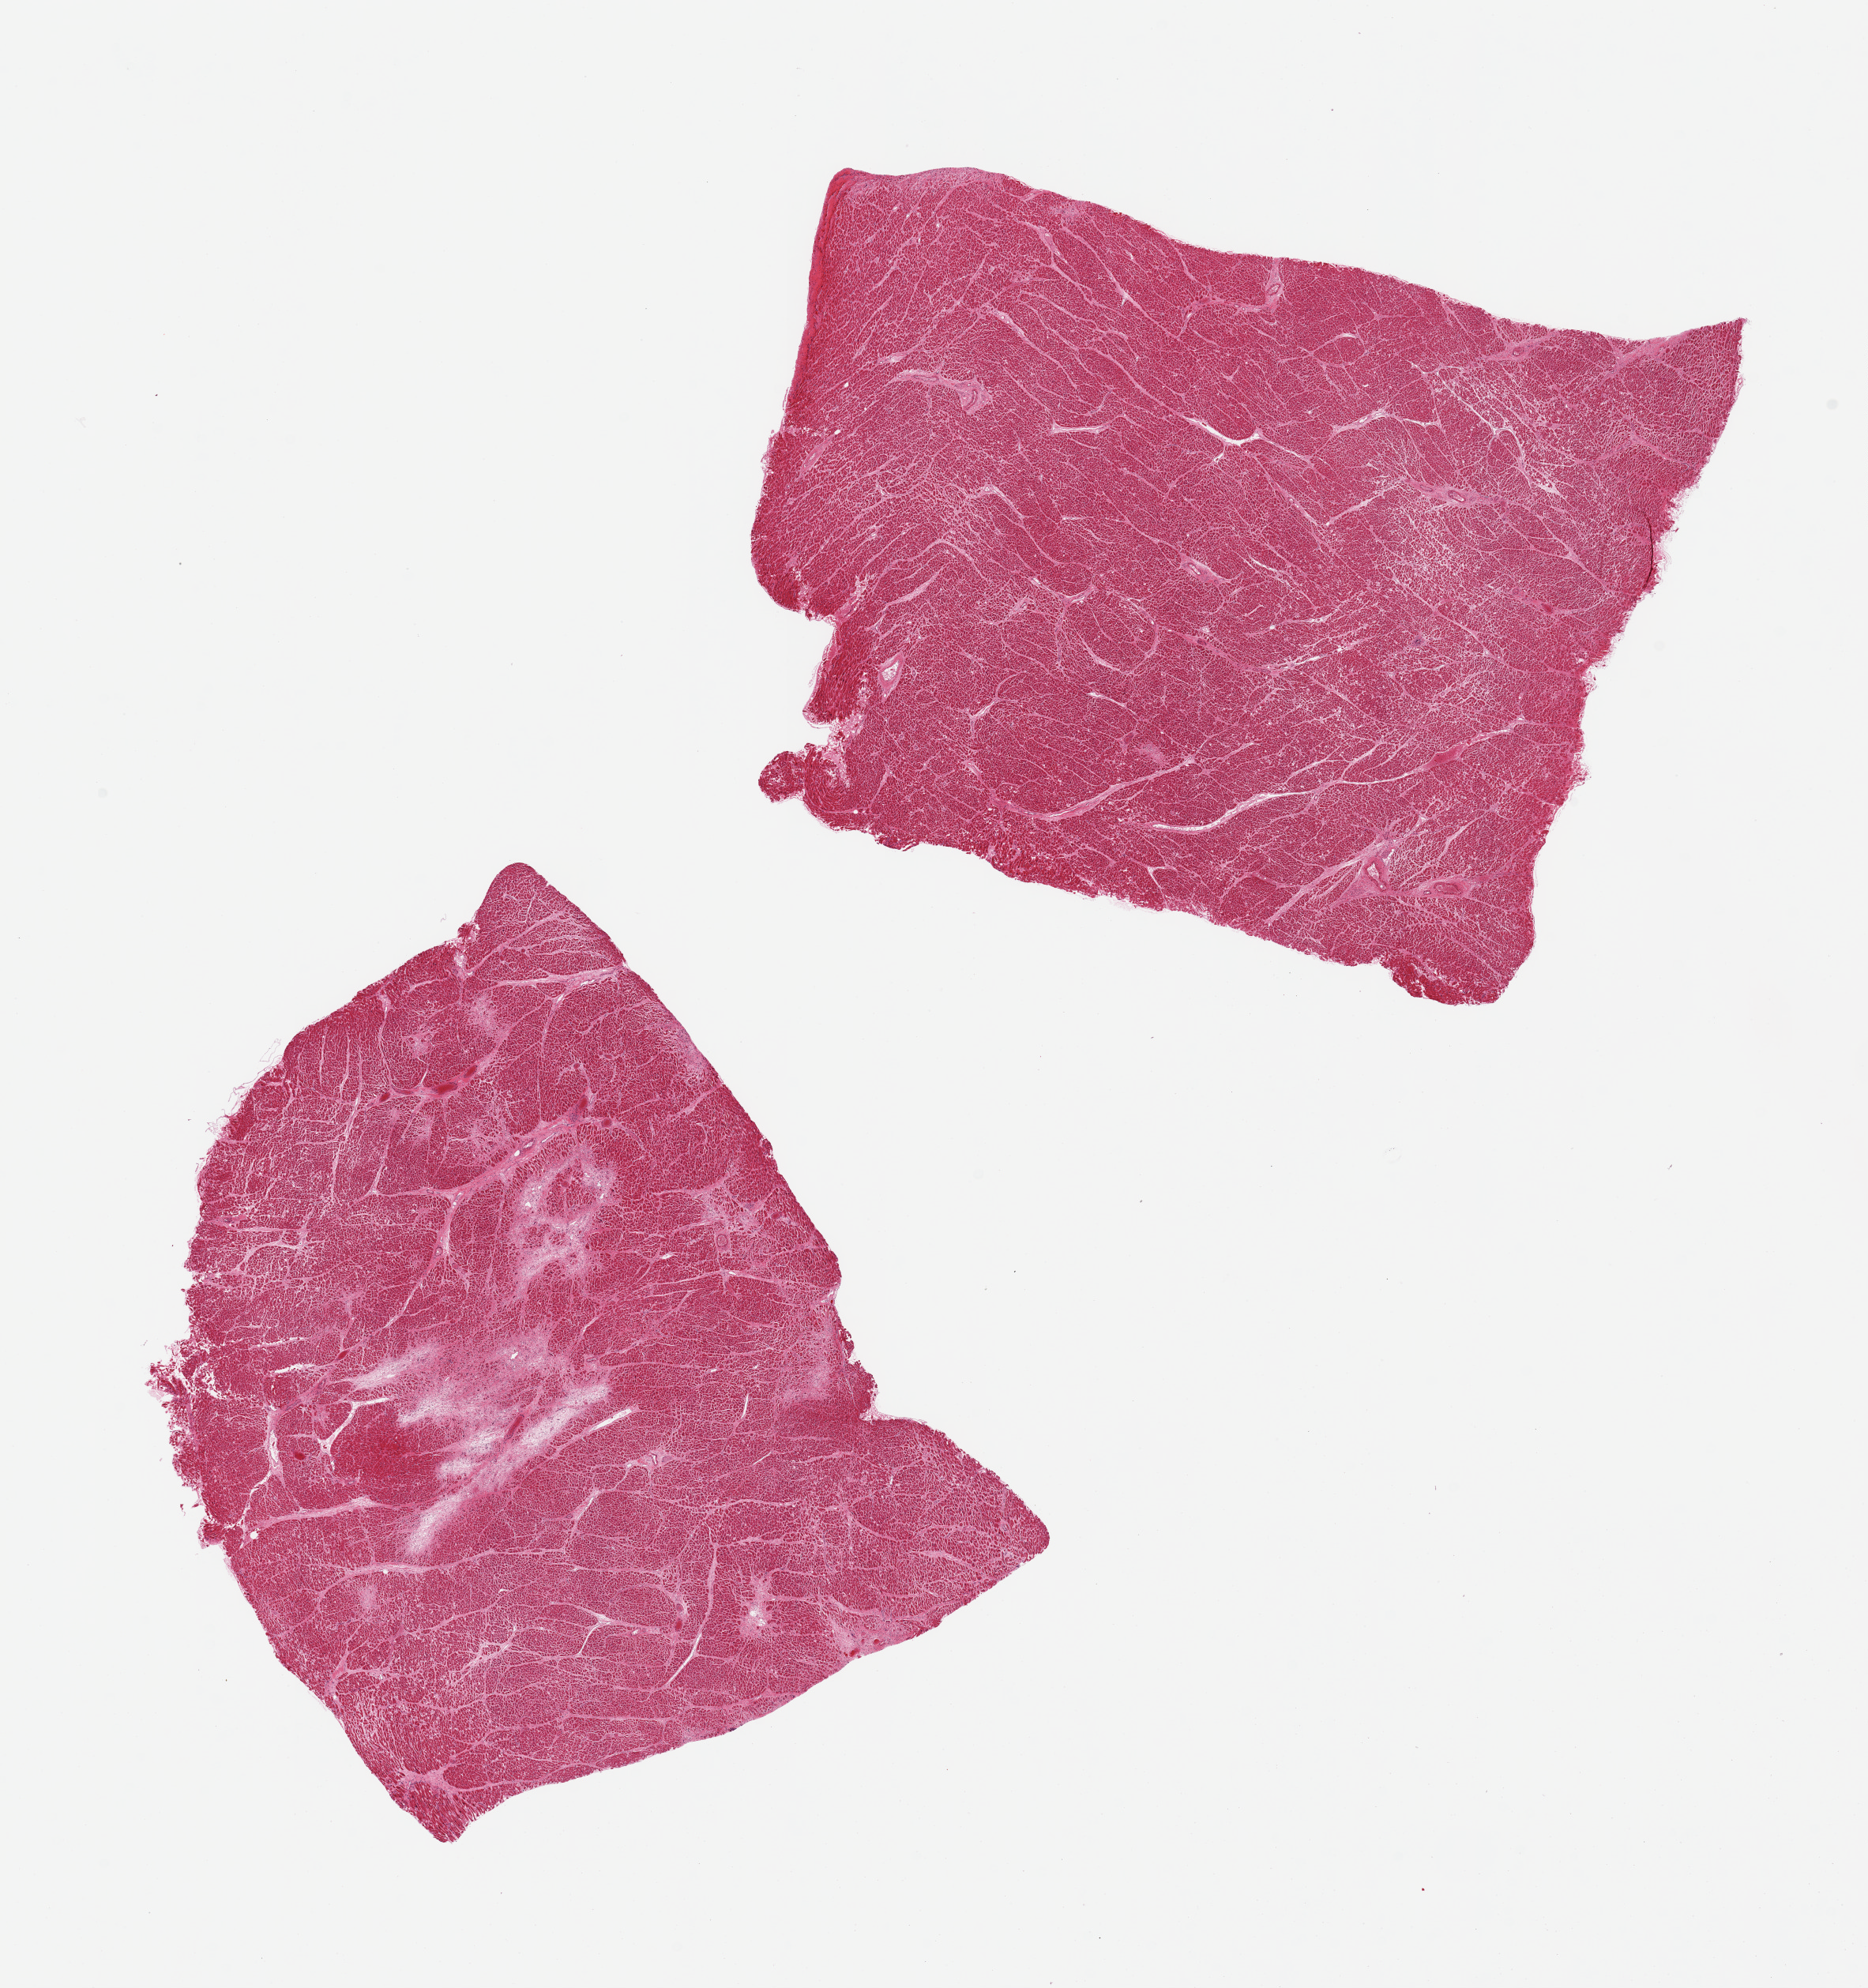
Digitized haematoxylin and eosin-stained section — low-resolution overview of the scanned area, about 18.7 x 19.9 mm; PAXgene-fixed paraffin-embedded (PFPE) section; target tissue: heart; donor tissue sample. Donor sex: male.
Review note (as recorded): 2 pieces; Patchy fibrosis (old infarct) and hypereosinophilia (very recent ischemia) in one piece.